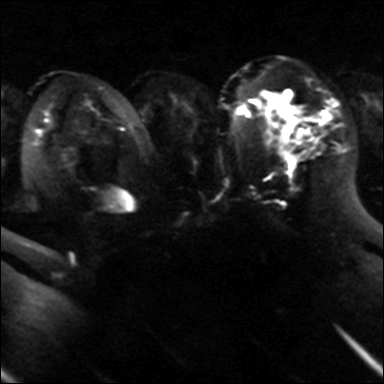
Breast MRI, one axial slice. Position 26 of 40 along the scan axis. Diffusion-weighted series; image 2 of 4 stored at this slice position (different b-values; order by instance number). 3 T. 4 mm slice thickness. 384 × 384 image matrix, field of view 320 × 320 mm. Female patient.
Structures marked on this image (outlined manually by an expert reader):
- tumour on diffusion-weighted imaging: bounding box [x1, y1, x2, y2] px = [298, 129, 307, 137]